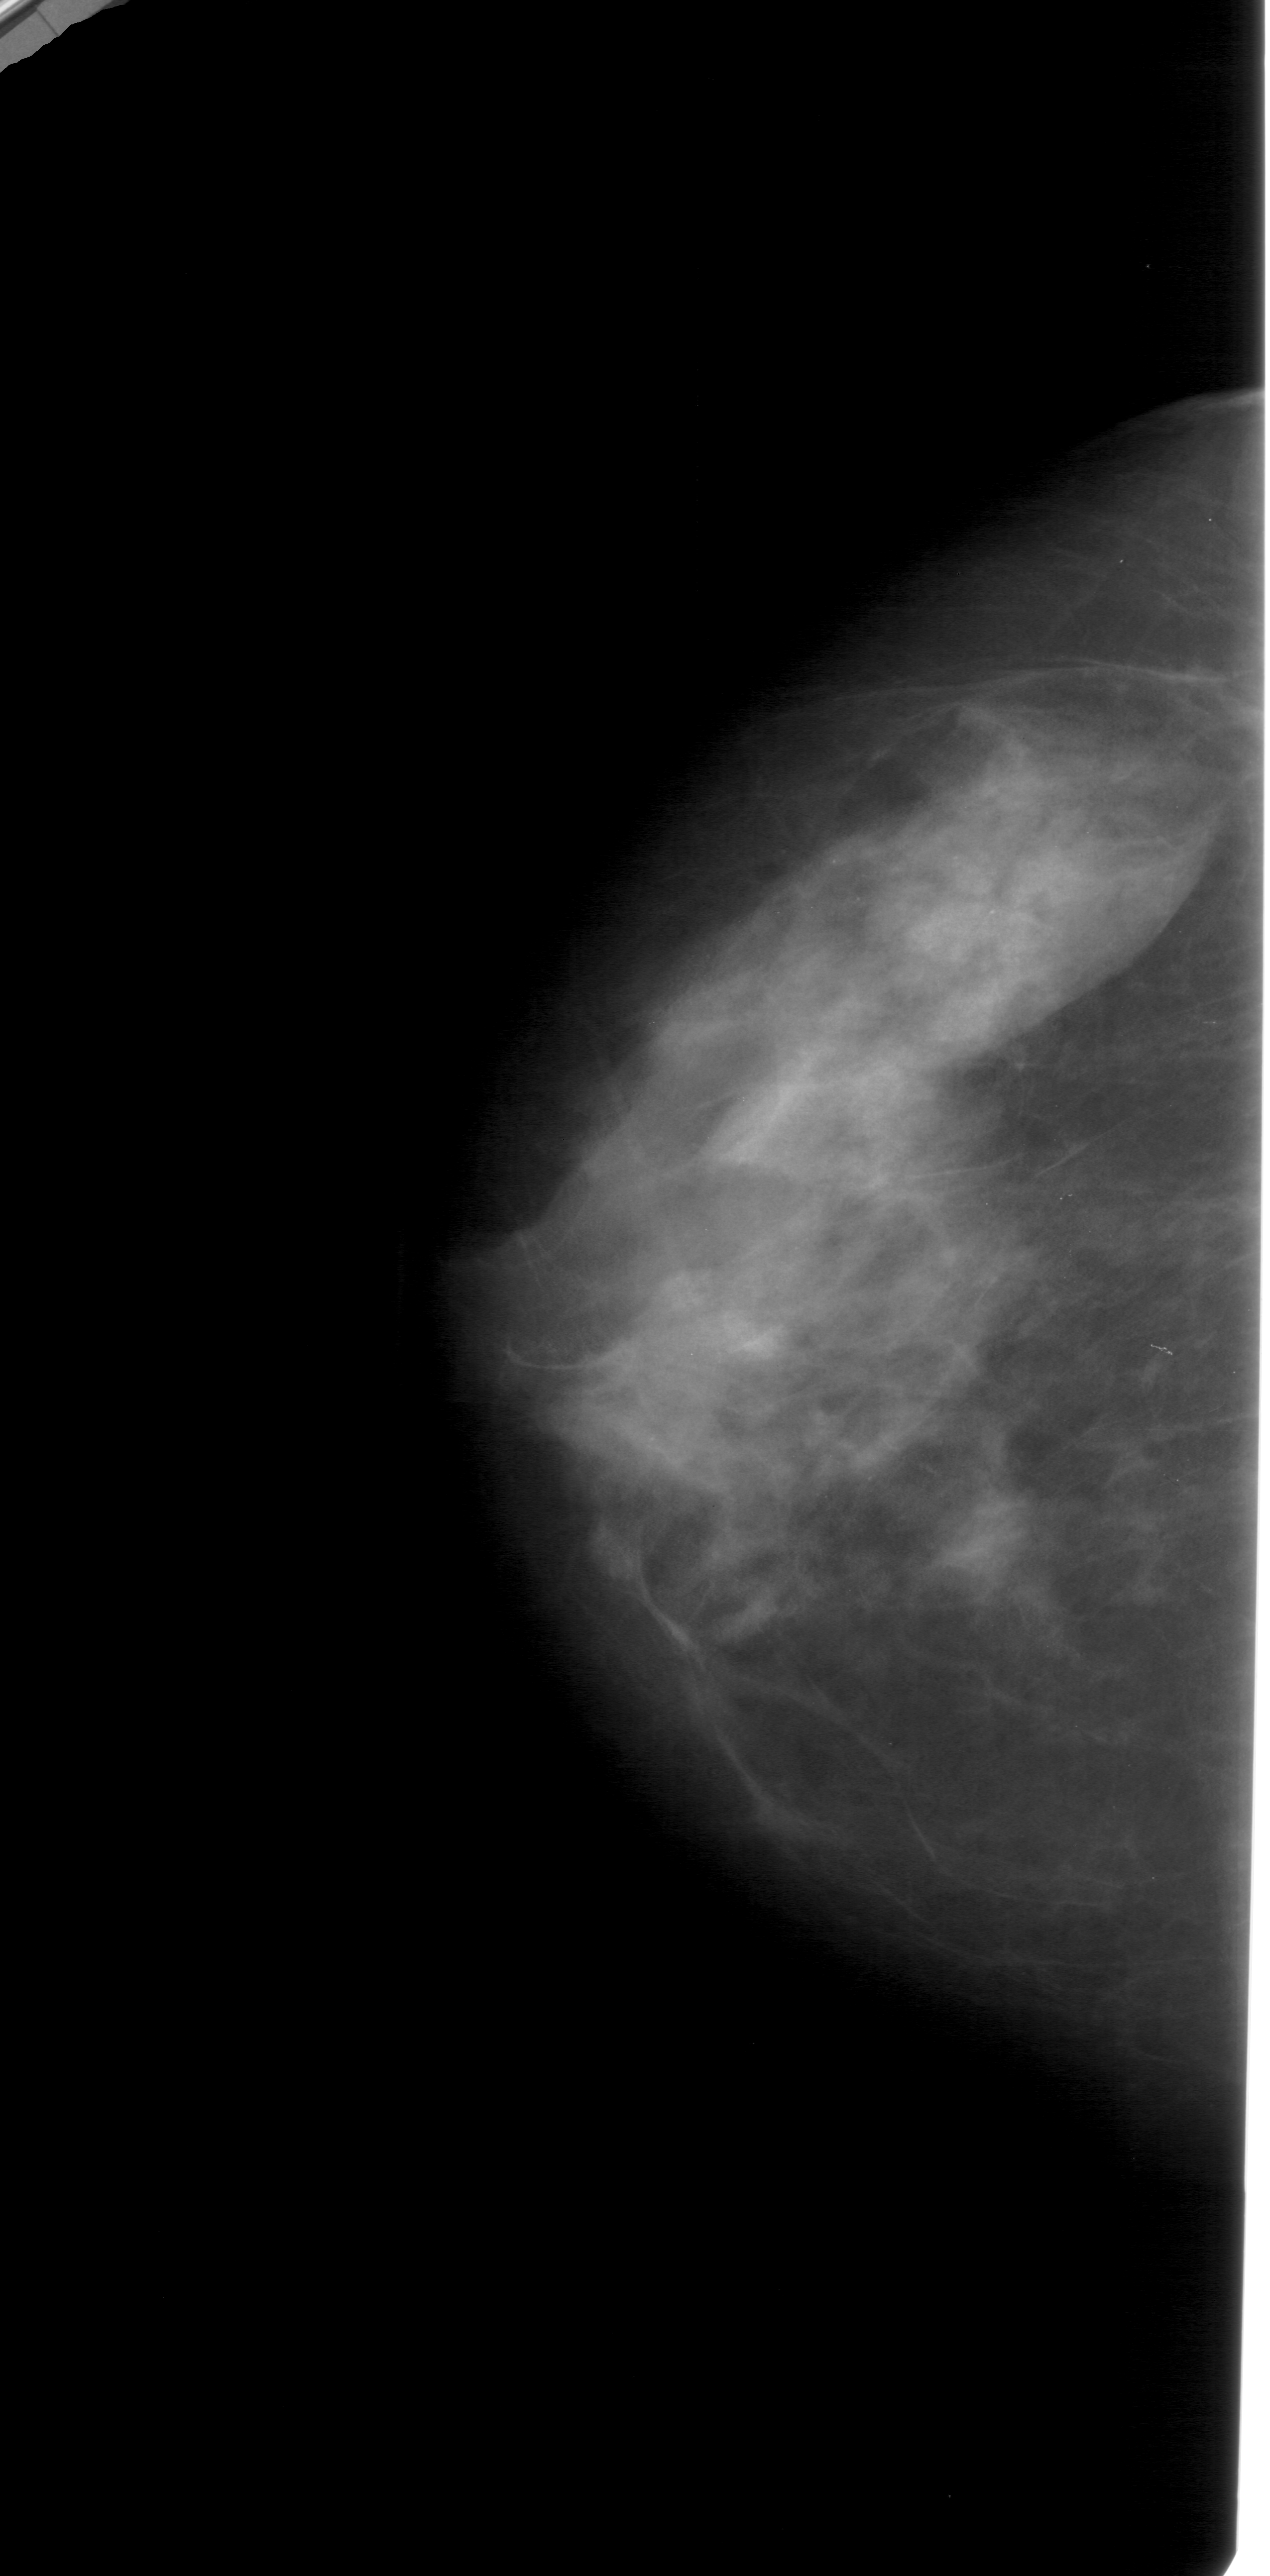
Digitized screen-film mammogram. Left breast. CC view. 1270 × 2576 image matrix.
Marked abnormalities (boxes around the expert regions of interest):
- calcifications, morphology punctate, distribution linear; BI-RADS assessment category 4; subtlety rating 1 on a 1 (subtle) to 5 (obvious) scale; pathology (as recorded): benign: box from (x=807, y=819) to (x=1051, y=932) px